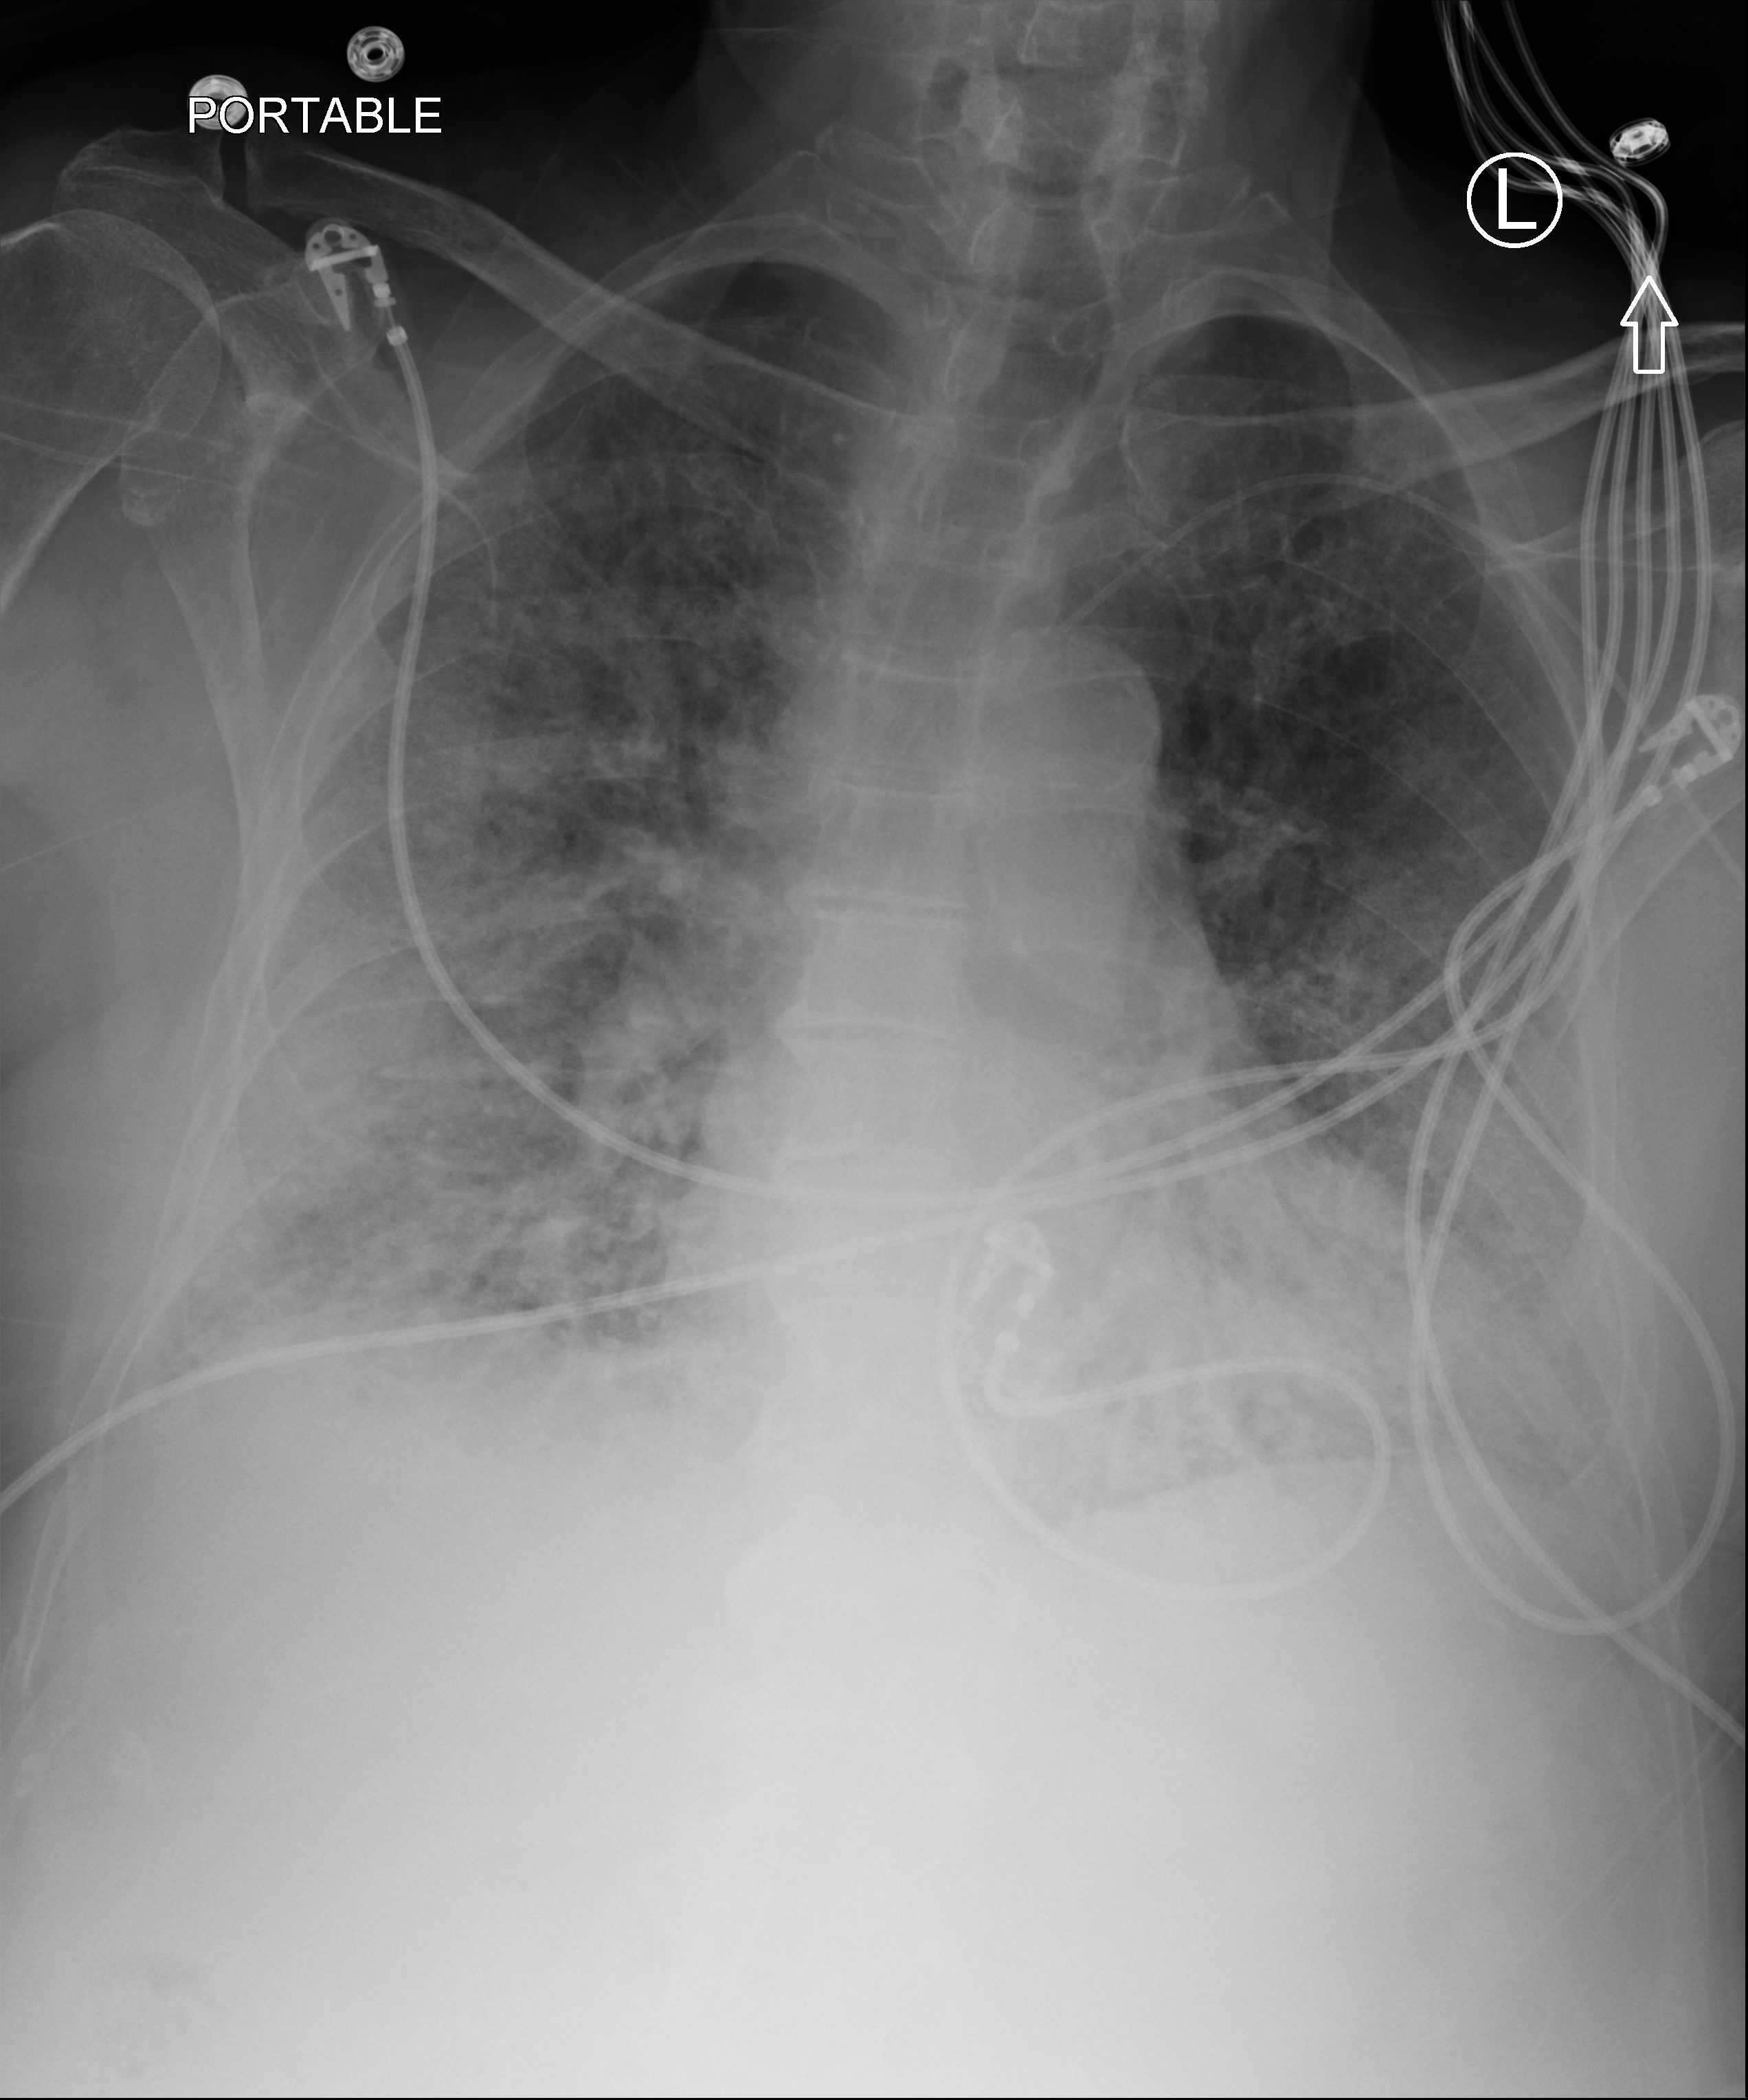
Chest X-ray (portable); anteroposterior (AP) projection. Patient hospitalised with COVID-19; male, aged 75–90 years.
From the hospital-stay record, not from the radiograph (when in the stay this image was taken is not recorded): other chronic lung disease (admission record): no.